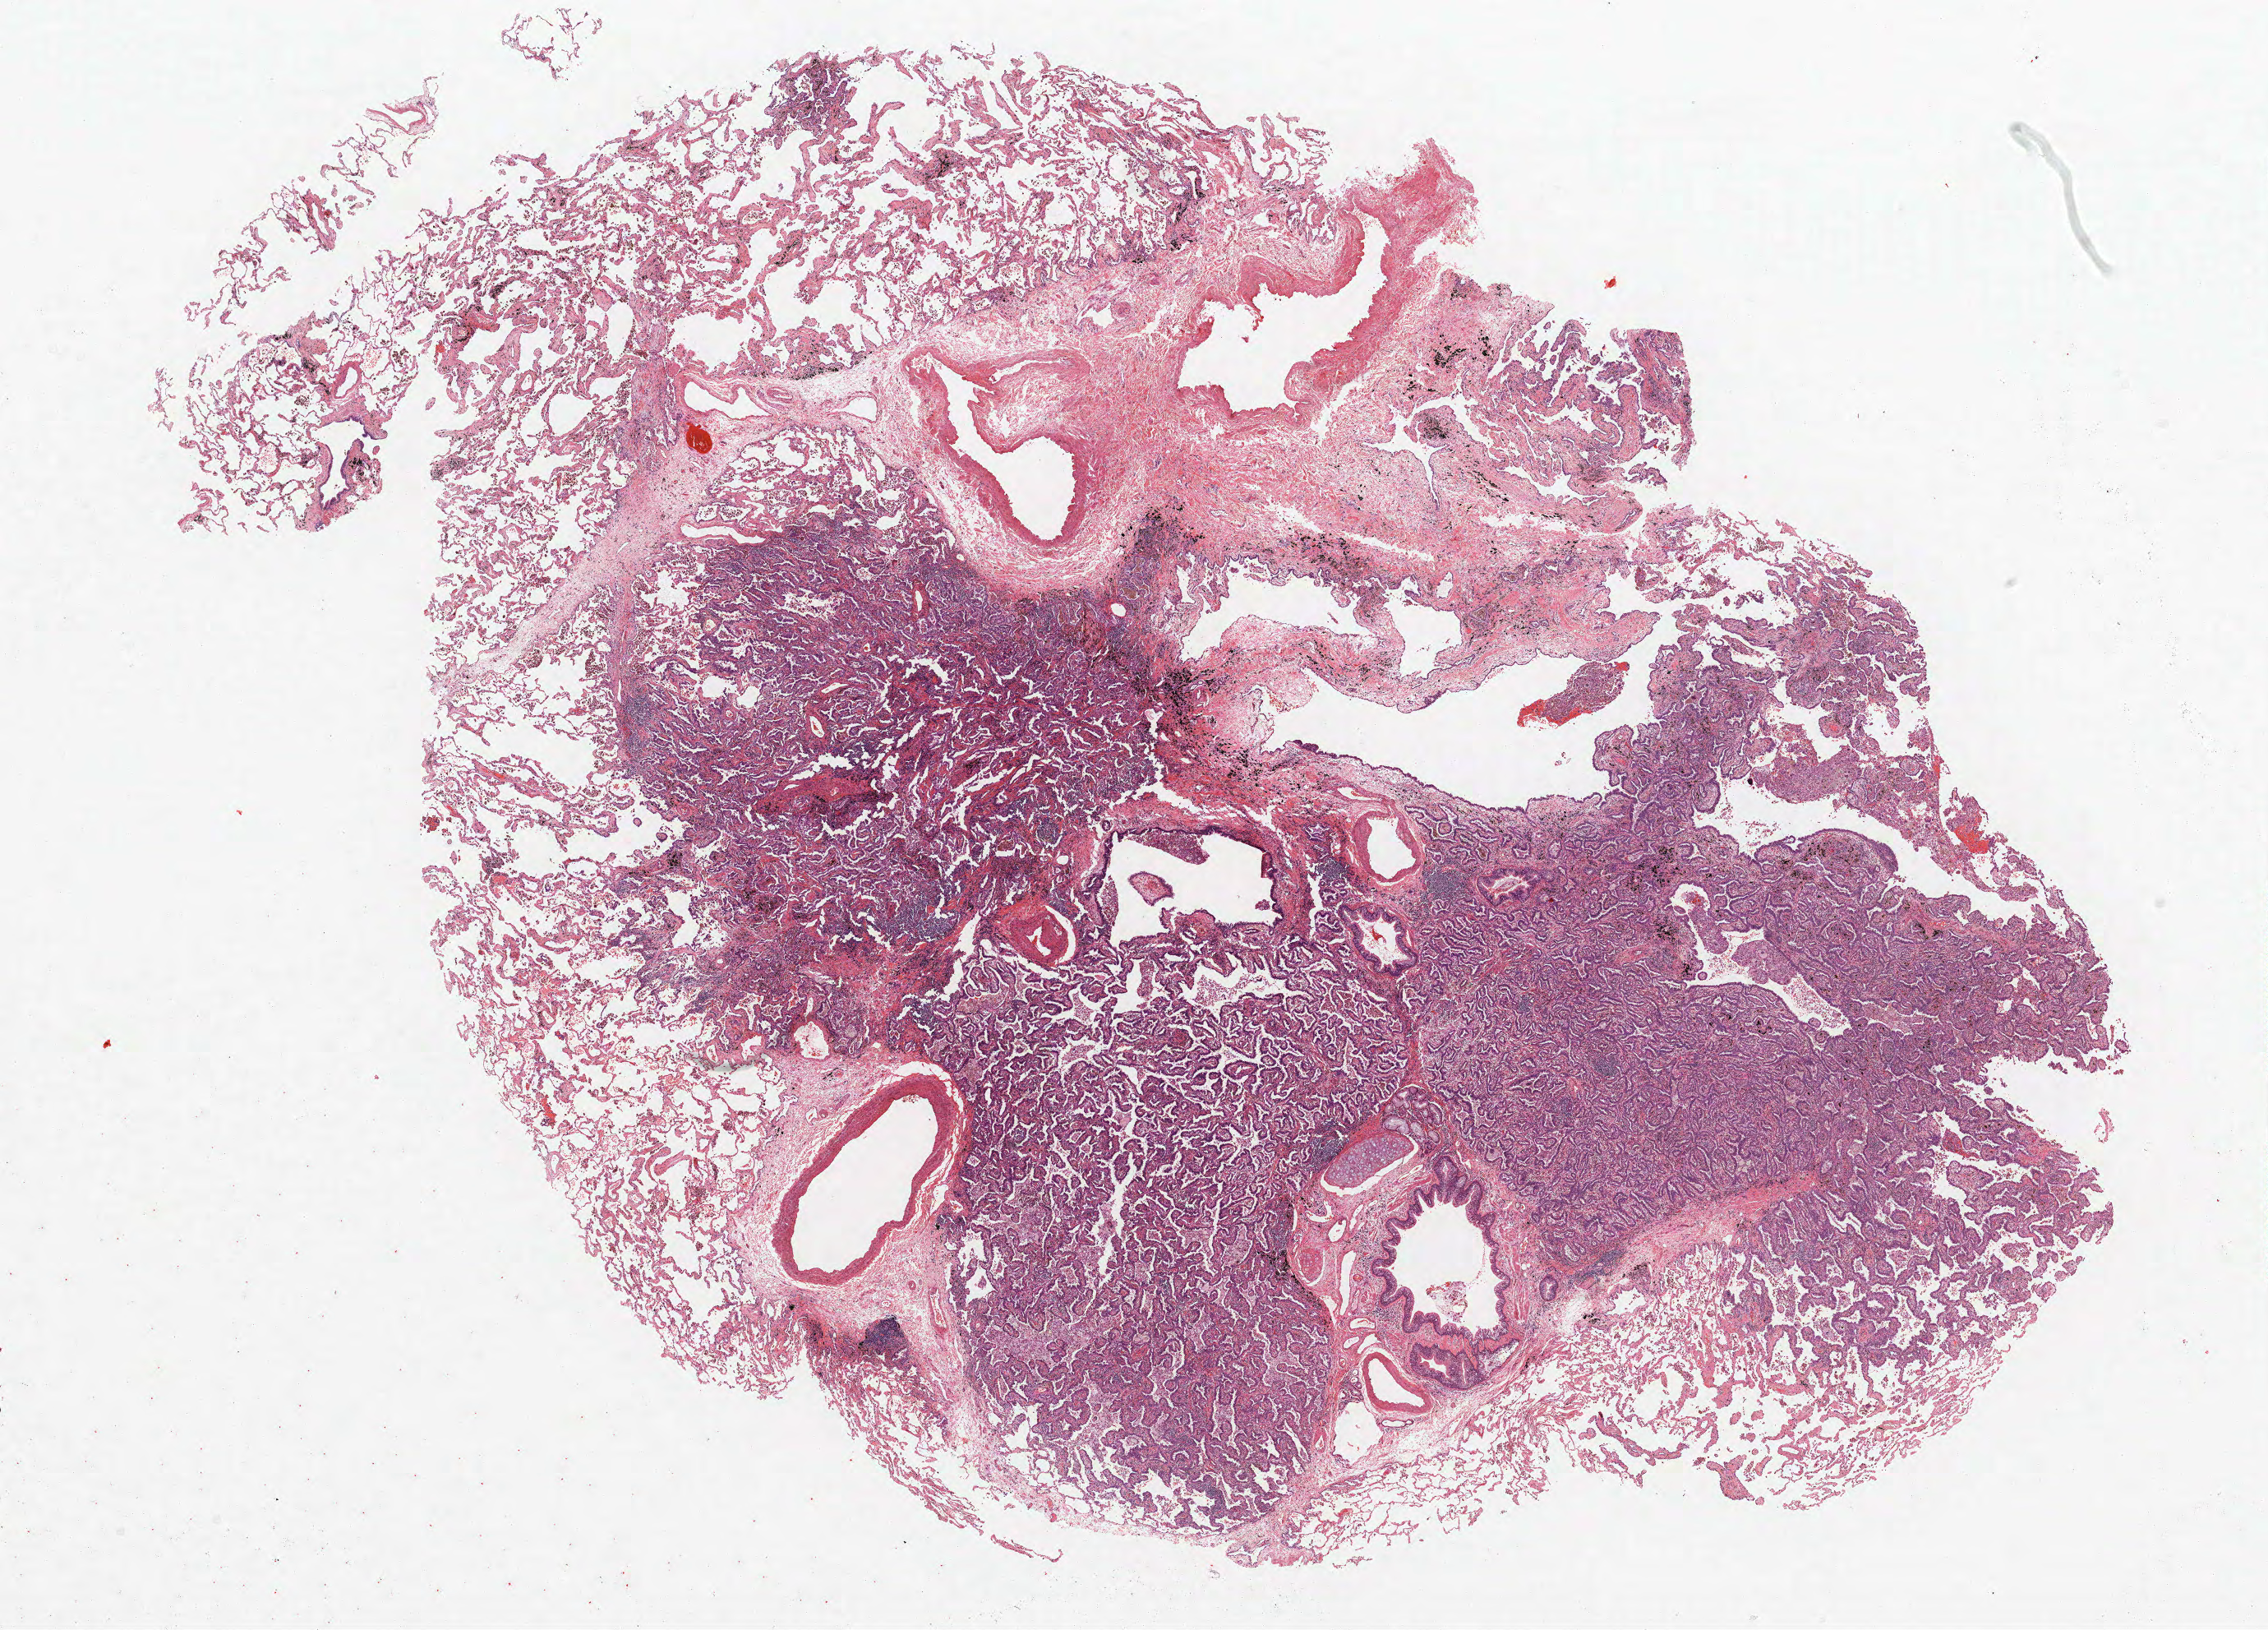
Whole-slide histology image, Hematoxylin and eosin (H&E) stained — a low-resolution overview of the entire scanned area, about 22.1 x 15.9 mm; FFPE section; lung tissue. Female patient, aged 61 at enrolment. Current smoker at enrolment. Grade: moderately differentiated (G2).
Participant's lung-cancer diagnosis: Adenocarcinoma, NOS (ICD-O-3 8140/3). Primary tumour location (clinical record): right upper lobe. Stage (AJCC 6th edition): IA. Tumour size (pathology): 20 mm.